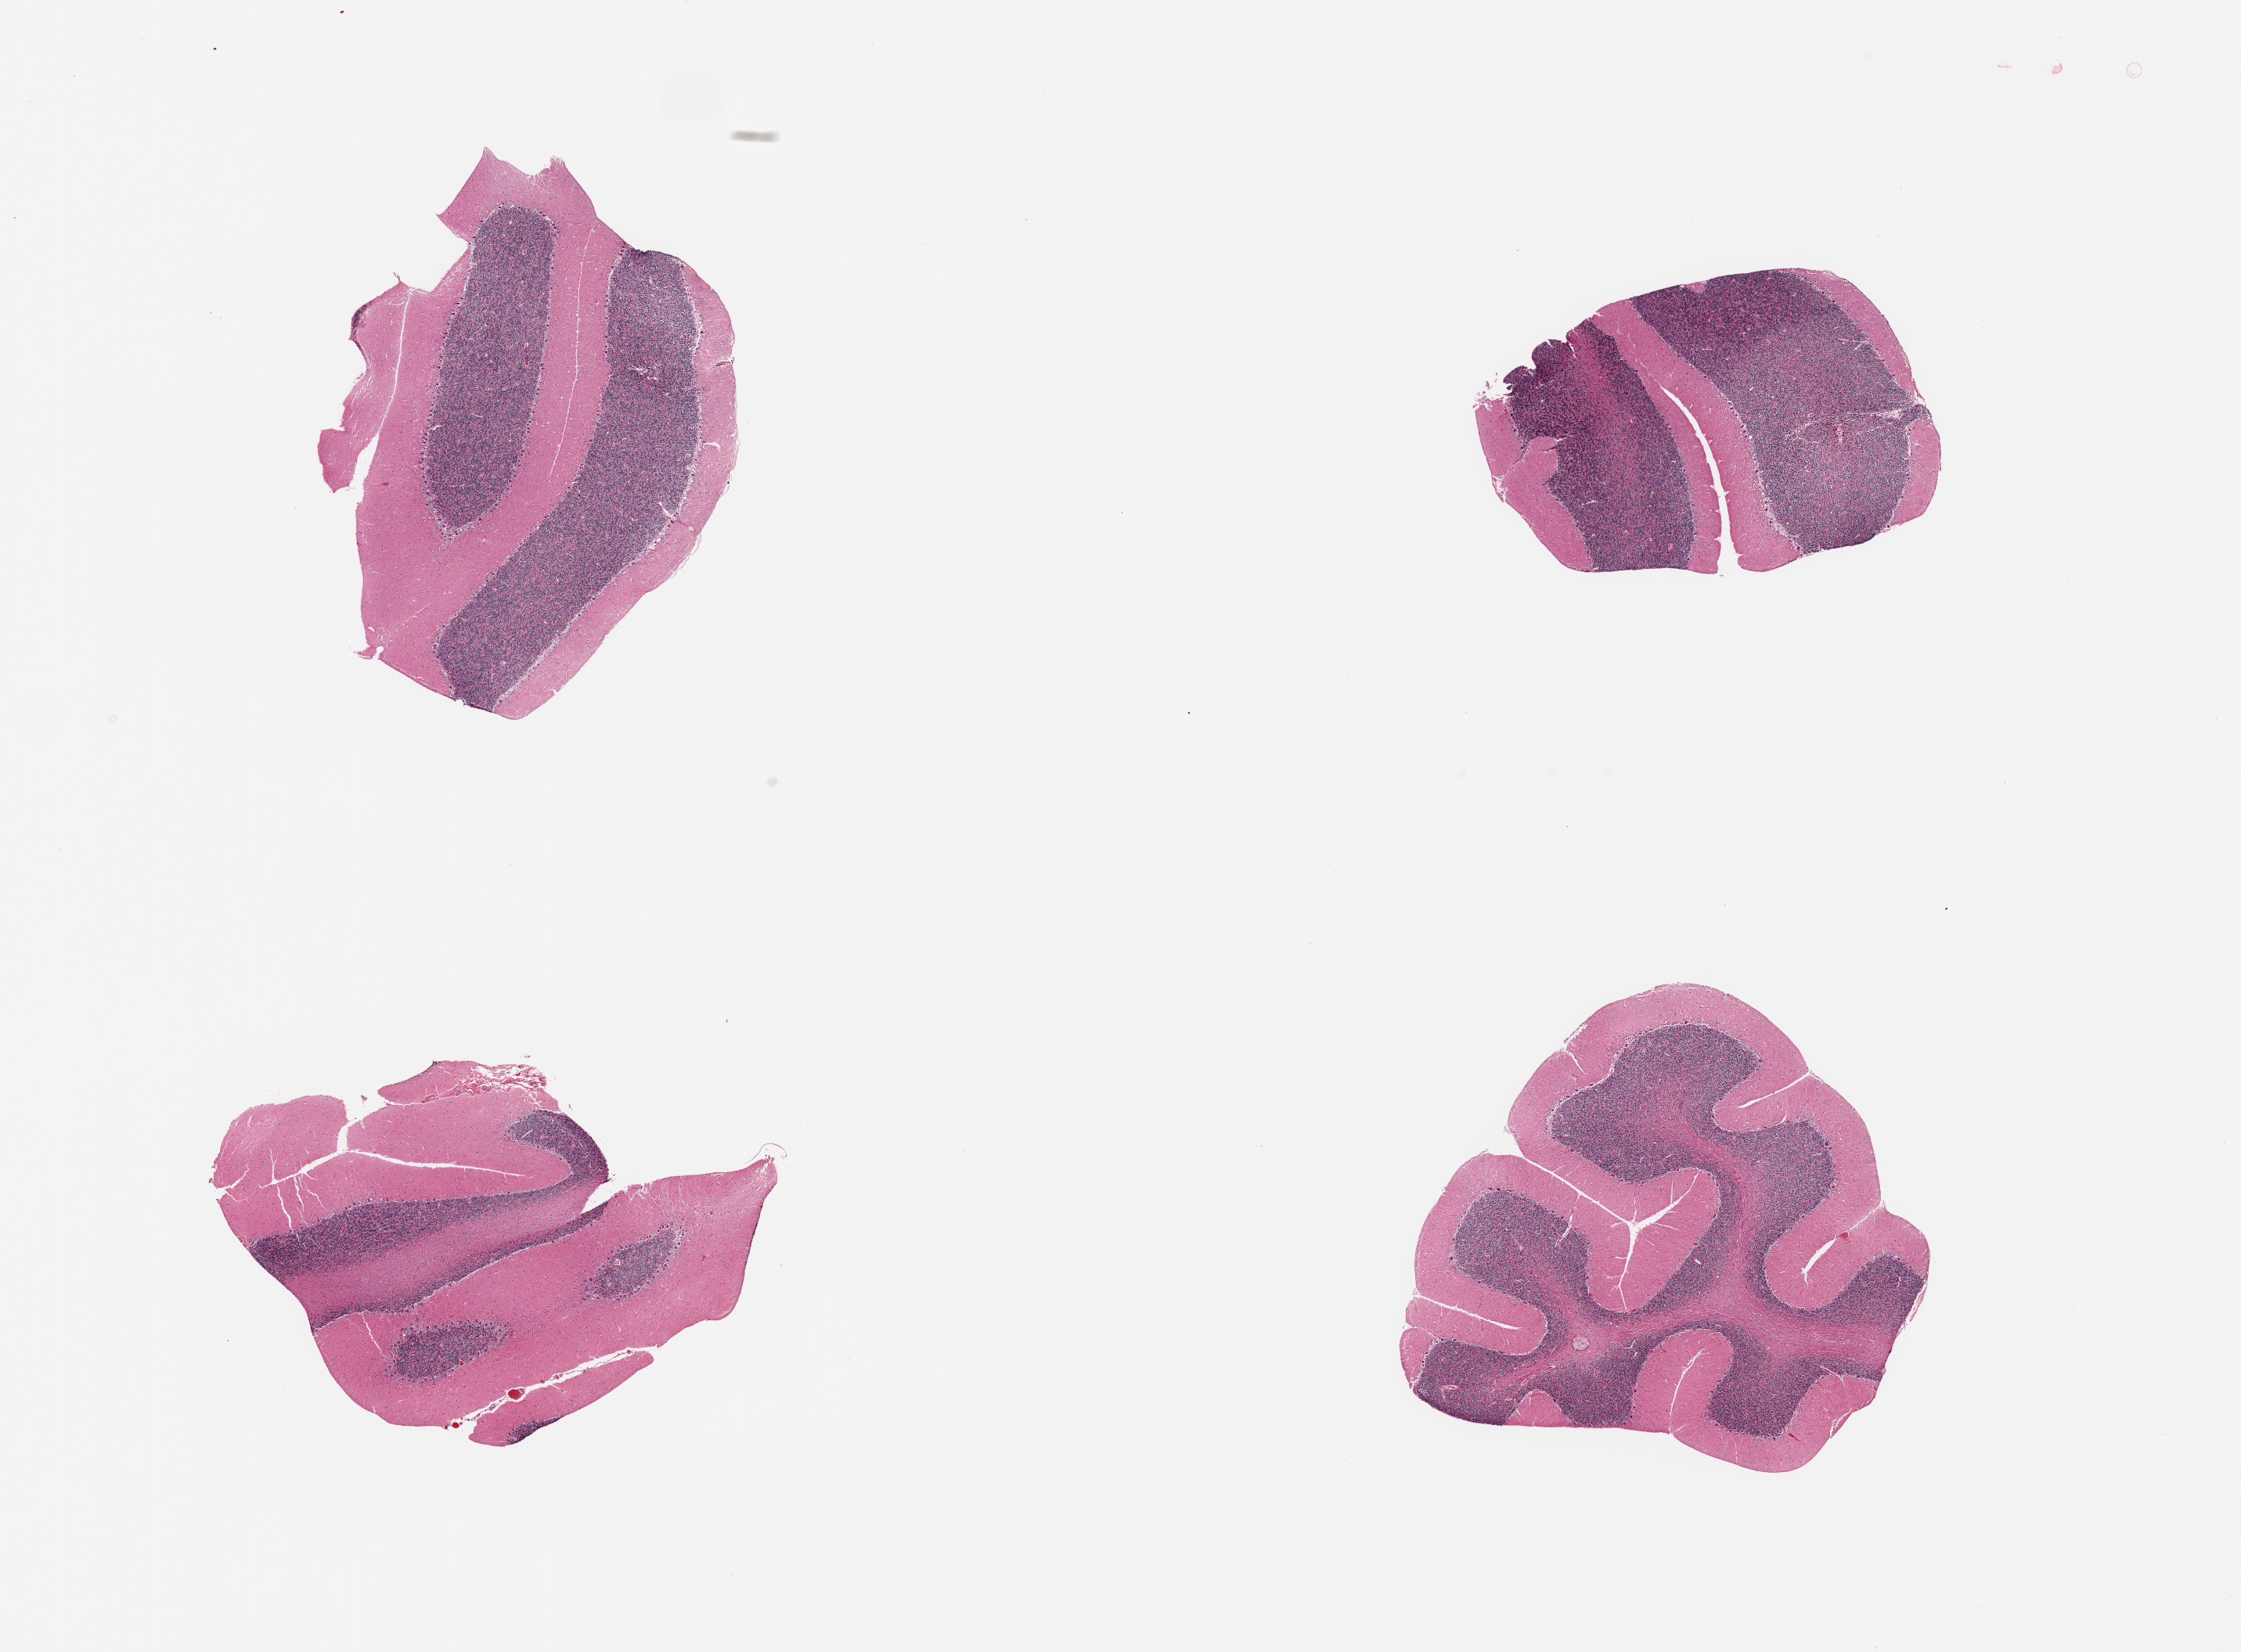
Hematoxylin and eosin (H&E) whole-slide image, brightfield — whole scanned area (about 22.6 x 16.7 mm) shown as a low-resolution overview, PAXgene-fixed paraffin-embedded (PFPE) section, target tissue: cerebellum, tissue donor sample.
Review note (as recorded): 4 pieces.